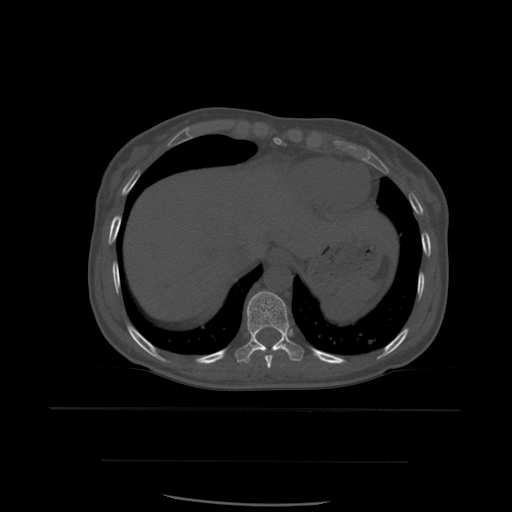
CT including the spine, one axial slice. Bone window (W 1800 / L 400 HU). 1.25 mm slice thickness. 512 × 512 image matrix, field of view 392 × 392 mm. Patient age 48 years. From the clinical record (not read from this slice): primary cancer: lung.
Outlined on this slice (semi-automatically segmented with operator editing):
- T10 vertebra: box from (x=236, y=291) to (x=304, y=364) px
- T9 vertebra: (x=264, y=348)–(x=285, y=369)